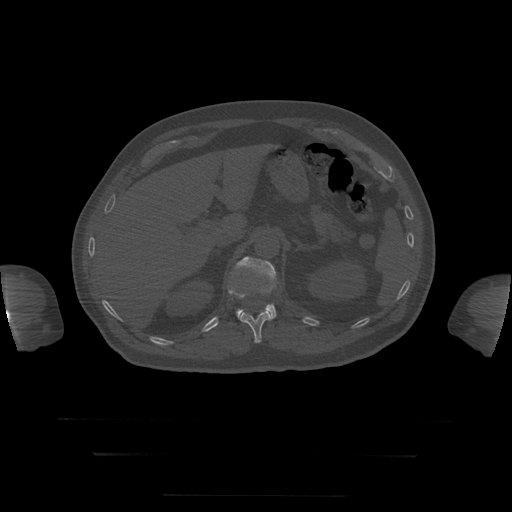
CT including the spine, one axial slice. Position 64 of 397 along the scan axis. Reconstruction kernel STANDARD. Bone window (W 1800 / L 400 HU). 1.25 mm slice thickness. 512 × 512 image matrix, field of view 510 × 510 mm. Patient age 73 years. Case-level facts recorded for this patient, not image findings: primary cancer: prostate.
Structures marked on this image (semi-automatically segmented with operator editing):
- L1 vertebra: bounding box (x1, y1, x2, y2) in pixels: (235, 257, 277, 320)
- T12 vertebra: (228, 286, 271, 343)